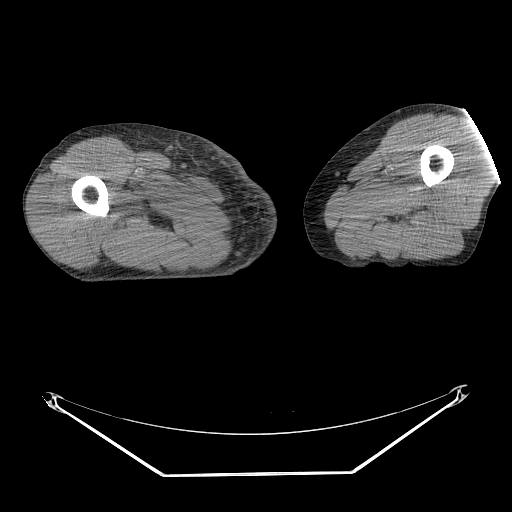
CT of an extremity soft-tissue mass (from a PET/CT study), one axial slice. Slice 235 of 311 in the series (ordered by position). 140 kVp. Soft-tissue window (W 400 / L 40 HU). 3.75 mm slice thickness. 512 × 512 image matrix. Male patient. Case-level facts recorded for this patient, not image findings: histological type: undifferentiated - pleiomorphic; grade: high; site of the primary tumour: right thigh.
Outlined on this slice (expert contour drawn on MRI and transferred to this co-registered scan by the dataset authors):
- gross tumour volume including surrounding oedema: bounding box [x1, y1, x2, y2] px = [135, 192, 200, 218]